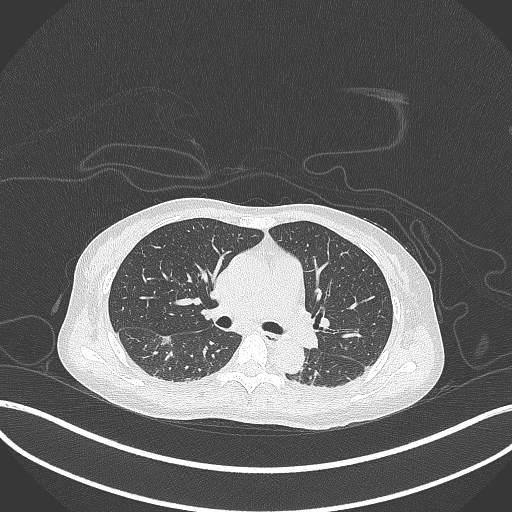
Chest CT, one axial slice. Slice 184 of 261 in the series (ordered by position). Reconstruction kernel B70f. 120 kVp. Lung window (W 1500 / L -600 HU). 1 mm slice thickness. 512 × 512 image matrix. Female patient, age 44 years. From the clinical record (not read from this slice): clinical TNM (as recorded): T1c N0 M0.
Structures marked on this image (bounding box drawn by a radiologist):
- lung tumour (recorded histology: adenocarcinoma): bounding box (x1, y1, x2, y2) in pixels: (158, 331, 174, 350)